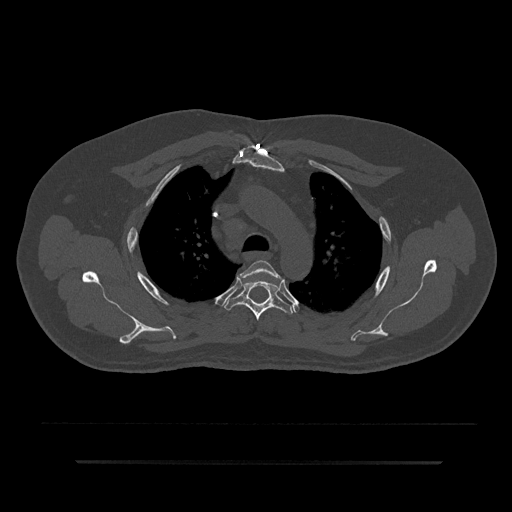
CT including the spine, one axial slice. Bone window (W 1800 / L 400 HU). 0.5 mm slice thickness. 512 × 512 image matrix, field of view 464 × 464 mm. Male patient, age 59 years. Case-level facts recorded for this patient, not image findings: primary cancer: bile ducts.
Outlined on this slice (semi-automatically segmented with operator editing):
- T3 vertebra: bounding box [x1, y1, x2, y2] px = [239, 260, 283, 281]
- T4 vertebra: [223, 274, 295, 321]